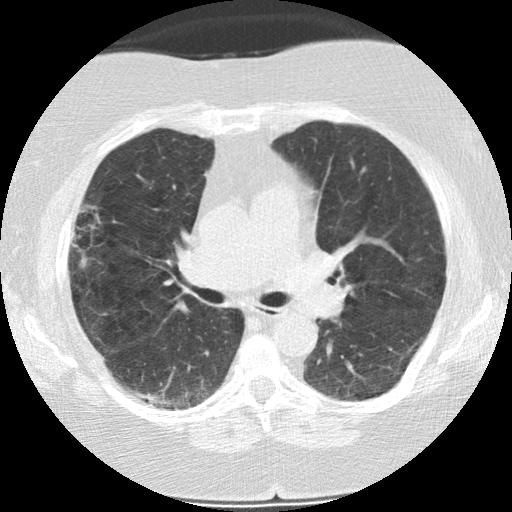
Low-dose screening chest CT, axial slice; baseline annual screen; lung window (W 1500 / L -600 HU); standard (soft-tissue) reconstruction kernel (STANDARD); 120 kVp. Female participant, aged 73 years at enrolment. Former smoker at enrolment.
- Expert-annotated lung lesion, bounding box <57,215,116,279> (left, top, right, bottom; pixels).
- Reader record for this screening exam (exam-level; its link to the box is not recorded): non-calcified nodule or mass ≥4 mm, right upper lobe, 21 × 14 mm, poorly defined margins, soft tissue attenuation.
- Participant outcome: lung cancer diagnosed 482 days after this screen (after the second annual screen) — bronchiolo-alveolar adenocarcinoma, NOS, right upper lobe, moderately differentiated (G2), stage IIIB (AJCC 6th edition), 21 mm at pathology.